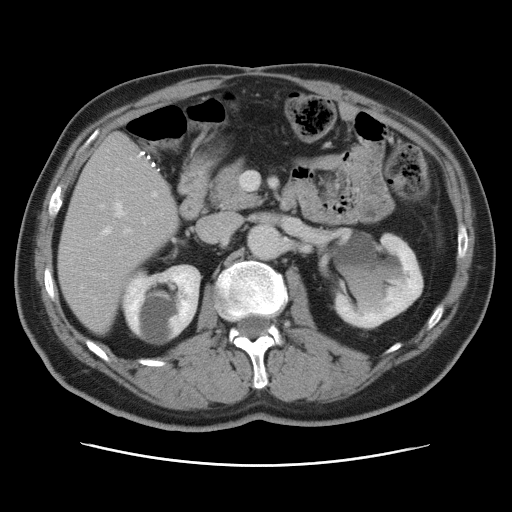
Contrast-enhanced abdominal CT, one axial slice; slice 35 of 80 in the series (ordered by position); 120 kVp; intravenous contrast given; soft-tissue window (W 400 / L 40 HU); 5 mm slice thickness; 512 × 512 image matrix, field of view 370 × 370 mm. Male patient, age 69 years. Case-level facts recorded for this patient, not image findings: diagnosis: colorectal cancer liver metastases, imaged before liver resection; multiple liver metastases: no; largest metastasis: 5 cm.
Outlined on this slice (outlined manually by an expert reader):
- hepatic veins: bounding box [x1, y1, x2, y2] px = [81, 203, 145, 288]
- liver: [59, 134, 178, 332]
- planned liver remnant (the part of the liver to remain after resection): [59, 197, 178, 332]
- portal vein (with intrahepatic branches): [101, 194, 155, 279]